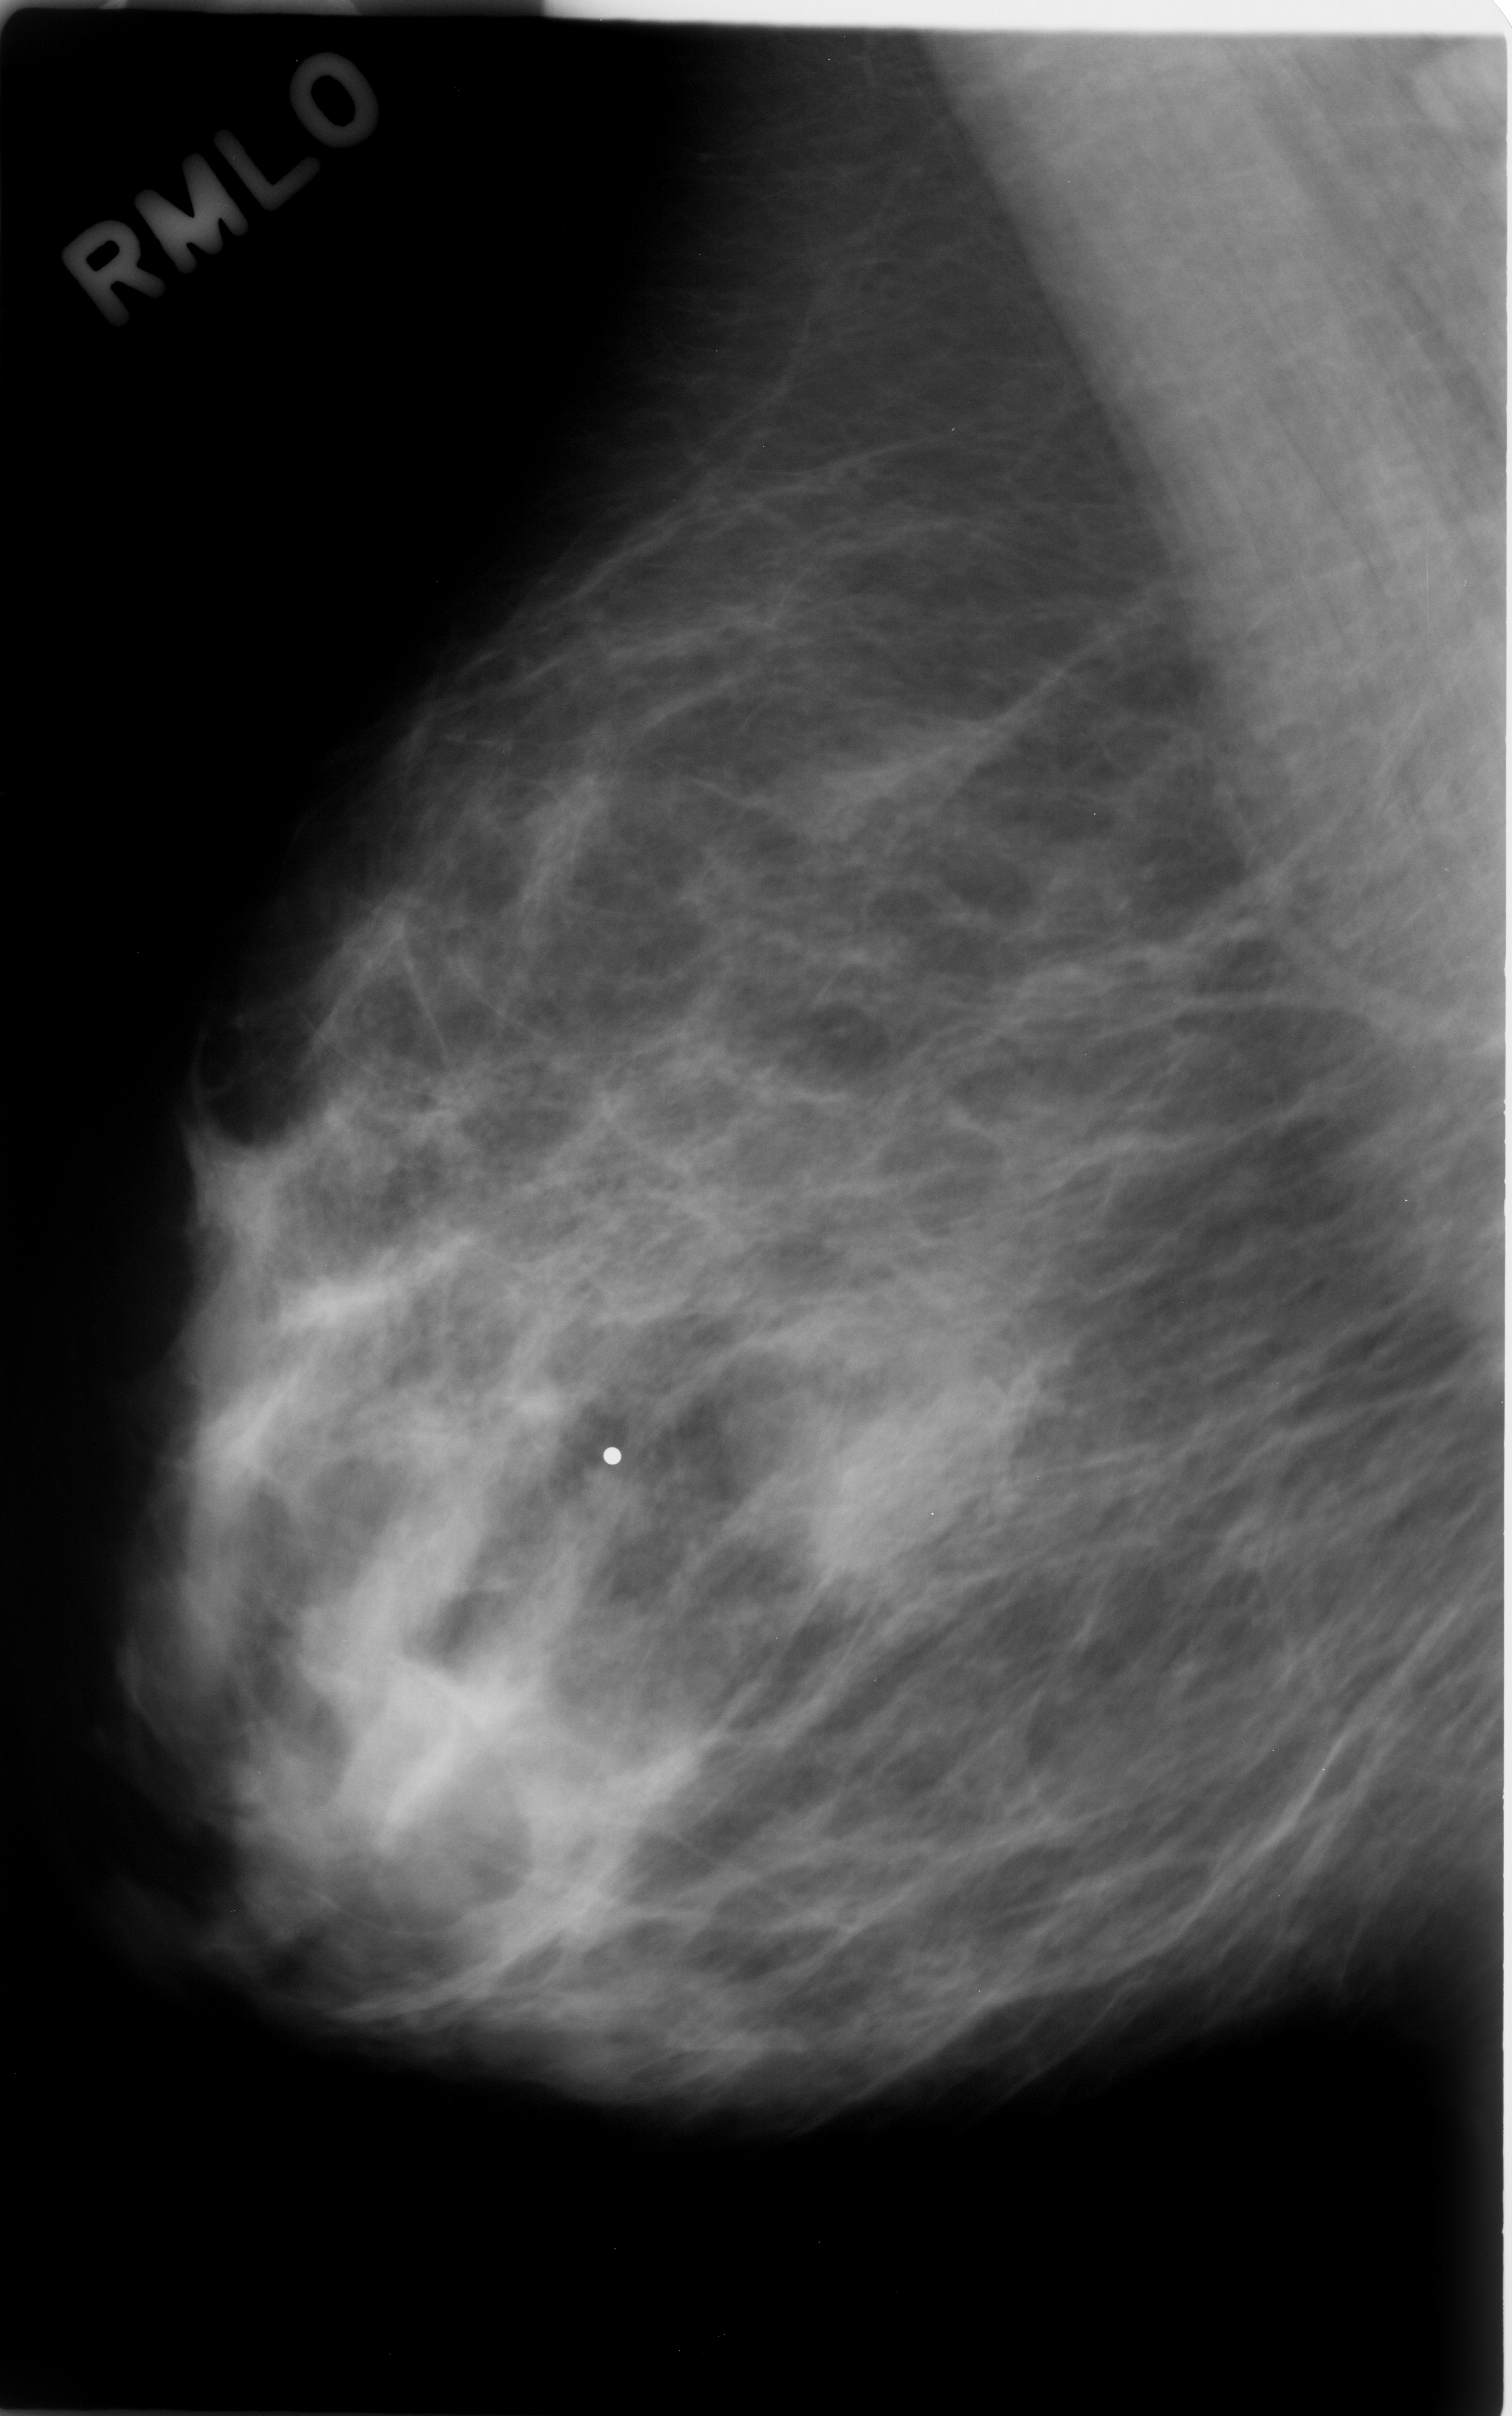
Mammogram (digitized film); right breast; mediolateral oblique (MLO) view; BI-RADS breast density category 2 (scale 1–4); 1512 × 2416 image matrix.
Expert-marked regions of interest on this film, with their recorded descriptors:
- mass, shape oval, margins obscured; BI-RADS assessment category 4; subtlety rating 3 on a 1 (subtle) to 5 (obvious) scale; pathology result (as recorded, not read from the image): benign: bounding box (x1, y1, x2, y2) in pixels: (780, 1363, 1000, 1566)